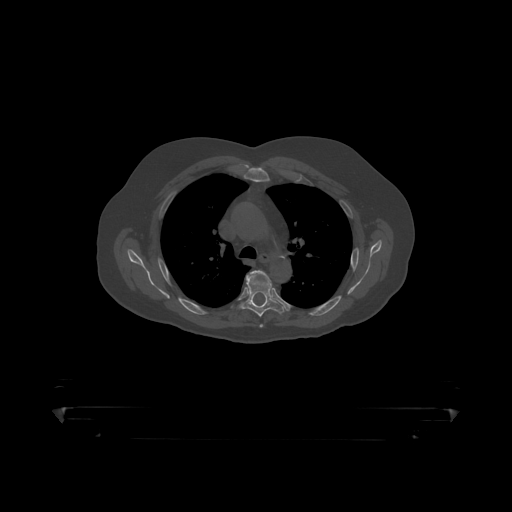
CT including the spine, one axial slice. Position 324 of 390 along the scan axis. Reconstruction kernel STANDARD. 120 kVp. Bone window (W 1800 / L 400 HU). 1.25 mm slice thickness. 512 × 512 image matrix. Male patient, age 60 years. Case-level facts recorded for this patient, not image findings: primary cancer: prostate.
Outlined on this slice (semi-automatically segmented with operator editing):
- T4 vertebra: bounding box (x1, y1, x2, y2) in pixels: (247, 271, 271, 283)
- T5 vertebra: (236, 277, 286, 318)